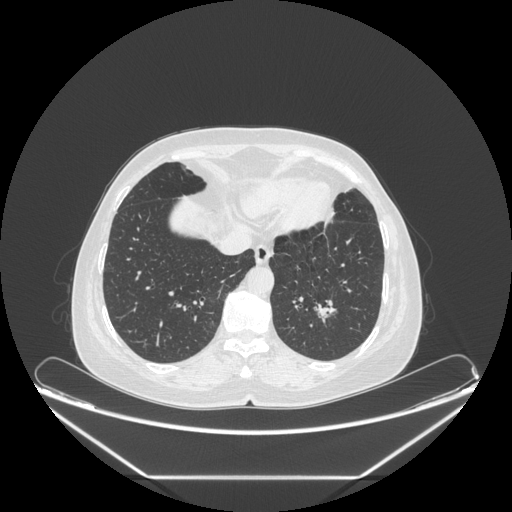
Chest CT, one axial slice; slice 68 of 241 in the series (ordered by position); reconstruction kernel STANDARD; 120 kVp; lung window (W 1500 / L -600 HU); 512 × 512 image matrix, field of view 451 × 451 mm. Patient: female, 63 years. From the clinical record (not read from this slice): clinical TNM (as recorded): T1c N0 M0; histopathological grade: G2-3.
Outlined on this slice (bounding box drawn by a radiologist):
- lung tumour (recorded histology: adenocarcinoma): bounding box (x1, y1, x2, y2) in pixels: (306, 293, 338, 331)